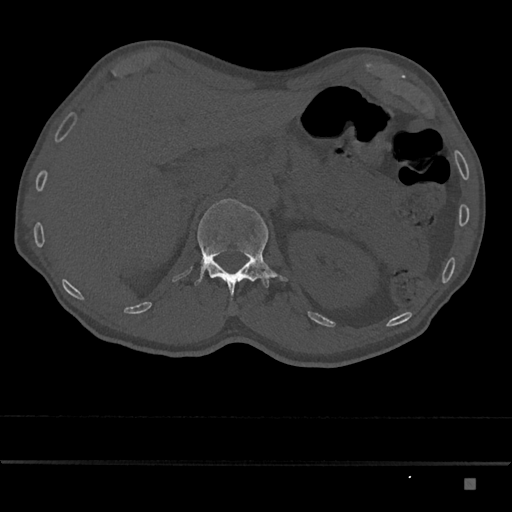
CT including the spine, one axial slice. Slice 547 of 797 in the series (ordered by position). Reconstruction kernel Br40s/3. 120 kVp. Bone window (W 1800 / L 400 HU). 512 × 512 image matrix, field of view 390 × 390 mm. Male patient, age 72 years. From the clinical record (not read from this slice): primary cancer: prostate.
Annotated regions visible in this slice (semi-automatic segmentation, software-assisted and operator-edited):
- L1 vertebra: bounding box (x1, y1, x2, y2) in pixels: (194, 199, 289, 300)